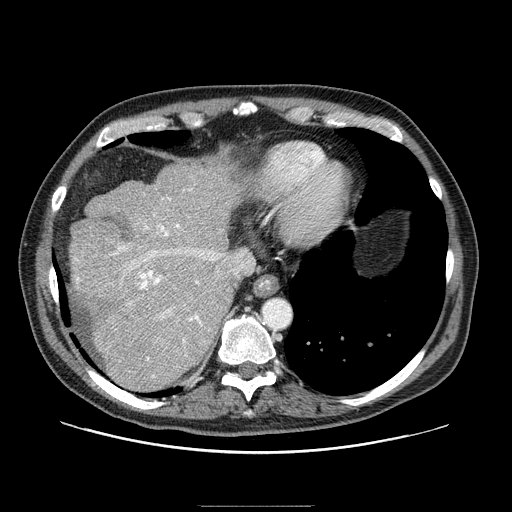
Contrast-enhanced abdominal CT (liver protocol), one axial slice; position 71 of 99 along the scan axis; one of 2 acquisitions stored at this slice position; soft-tissue window (W 400 / L 40 HU); 2.5 mm slice thickness; 512 × 512 image matrix, field of view 400 × 400 mm. Case-level facts recorded for this patient, not image findings: diagnosis: hepatocellular carcinoma (patient treated with transarterial chemoembolisation; whether this scan precedes or follows treatment is not stated here); TNM stage (as recorded): Stage-II; Child-Pugh class: A; tumour nodularity: multinodular; tumour size: 3.2 cm.
Structures marked on this image (semi-automatically segmented with operator editing):
- abdominal aorta: box from (x=262, y=298) to (x=291, y=328) px
- liver parenchyma outside the tumour (the mass and vessels are separate outlines, so this box may not span the whole liver): (x=68, y=162)–(x=240, y=388)
- liver vessels: (x=76, y=189)–(x=225, y=378)